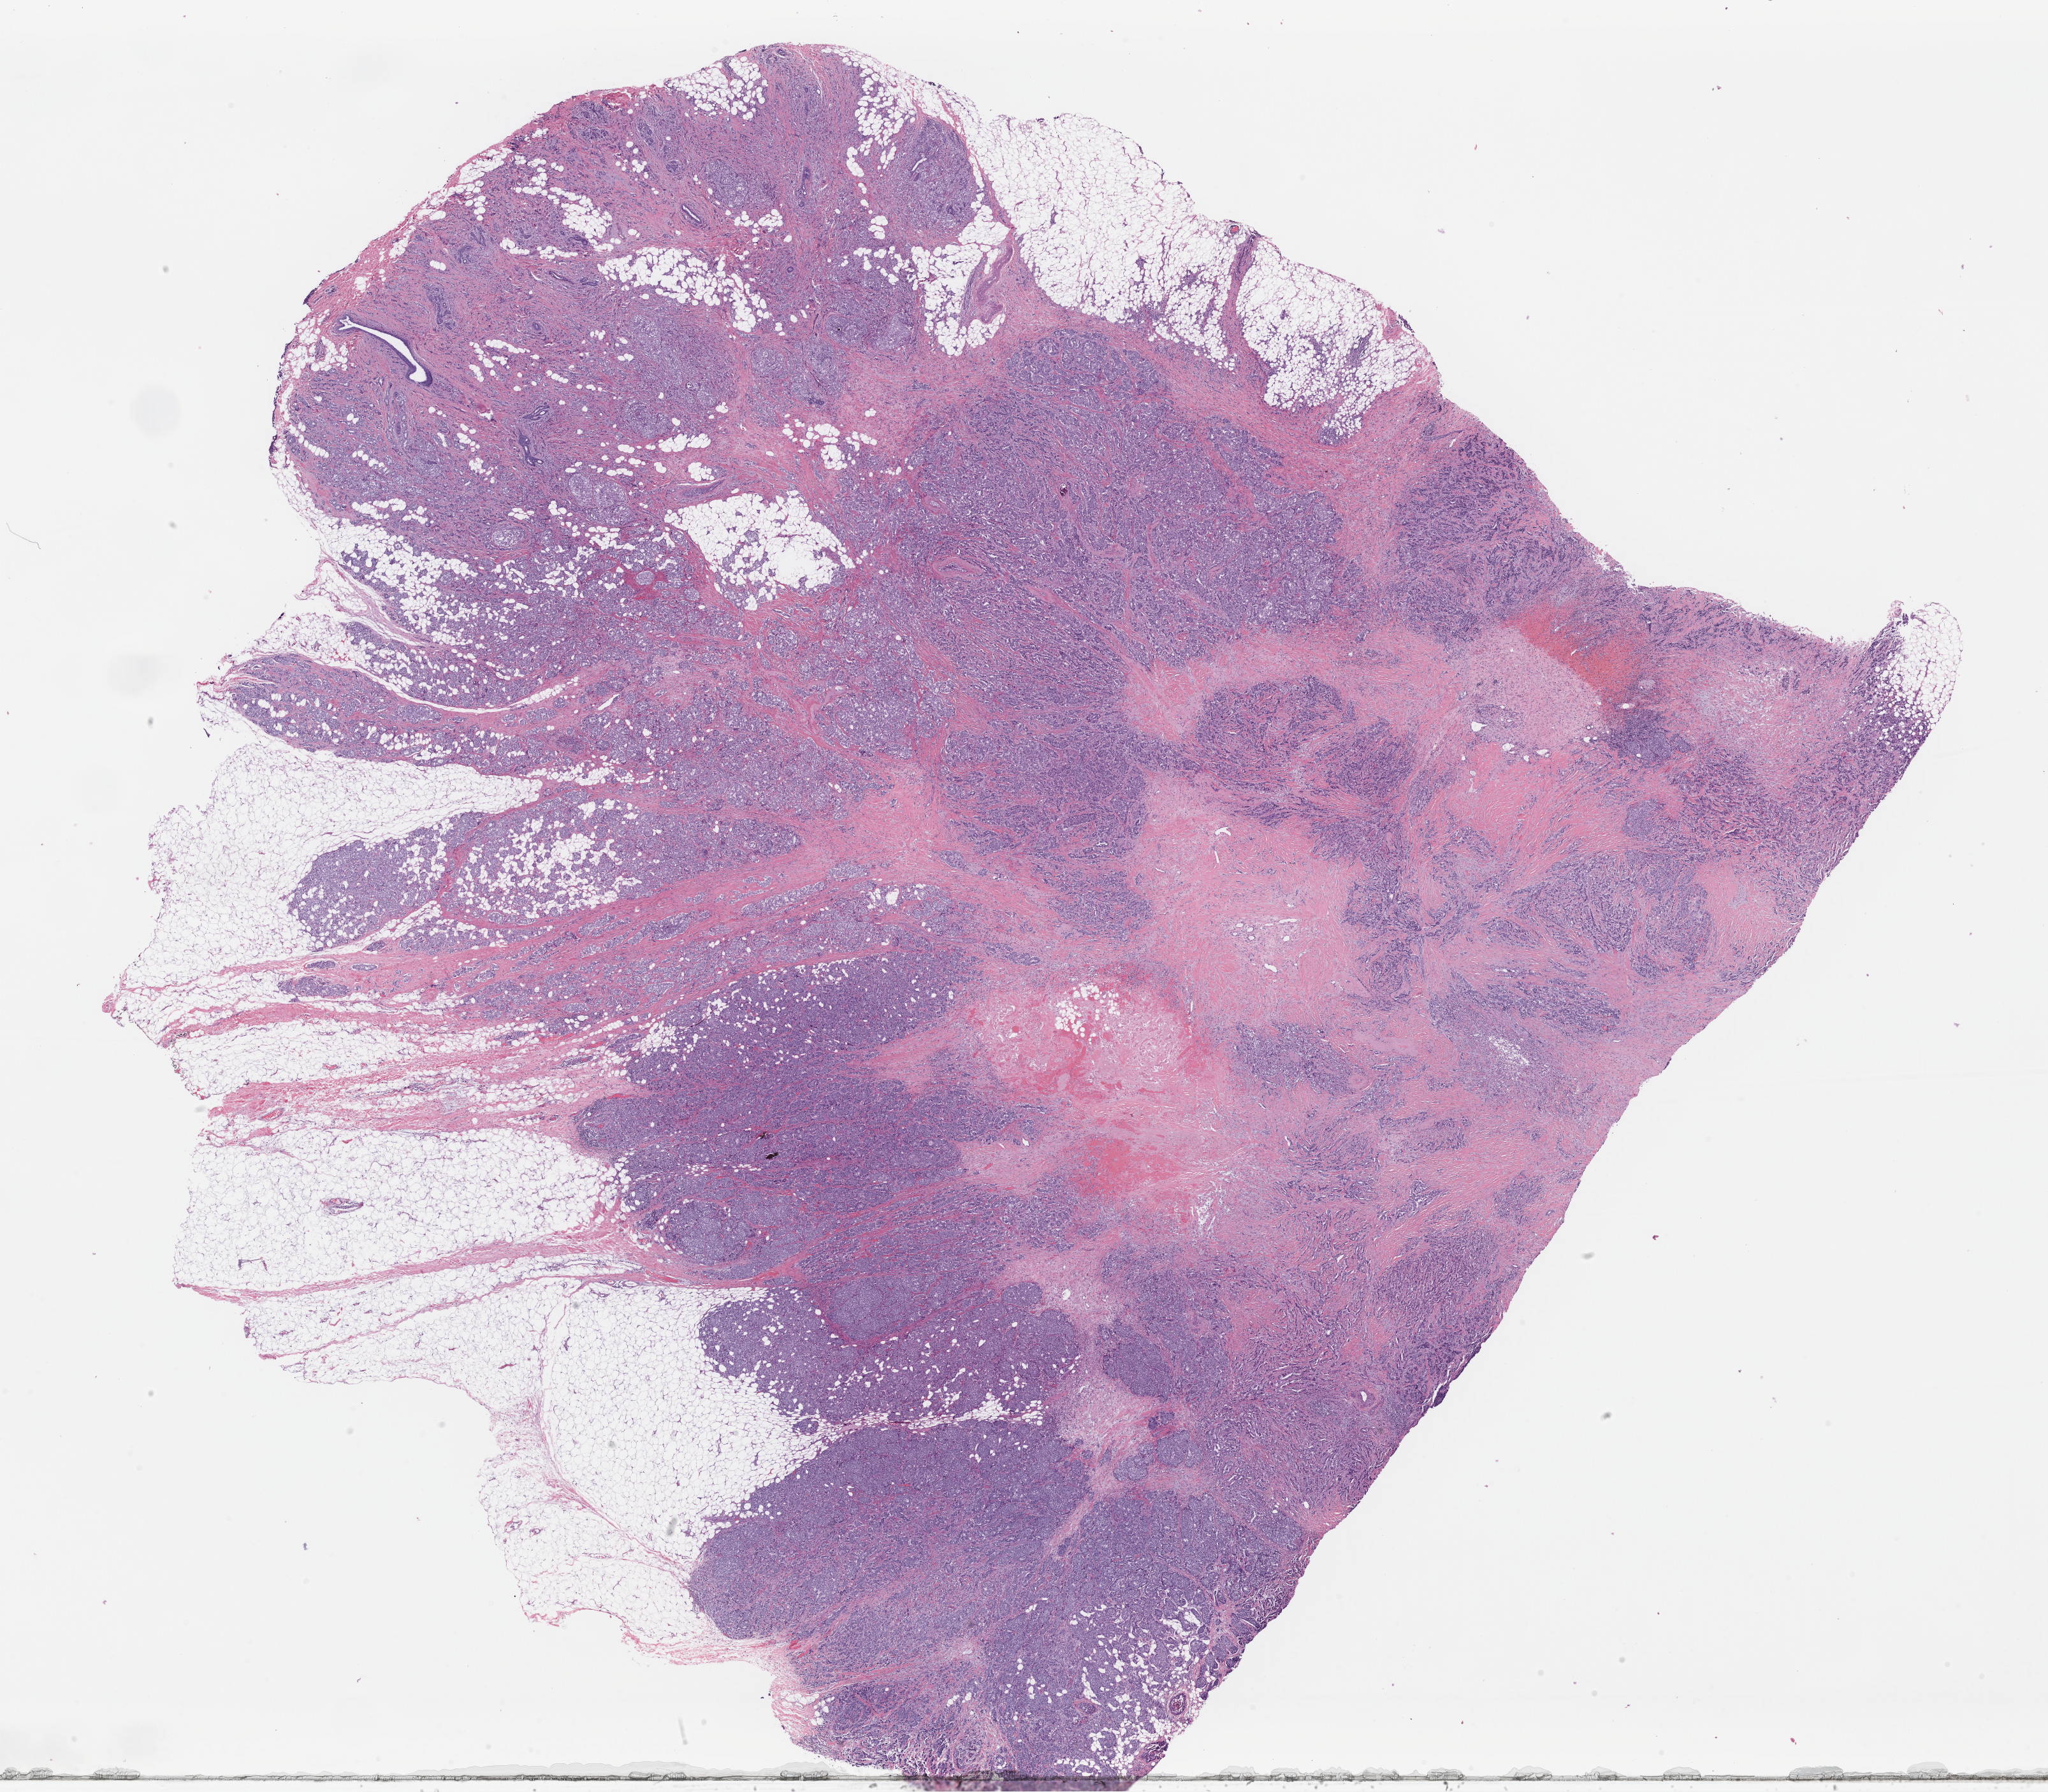
Hematoxylin and eosin (H&E) stained whole-slide image, low-resolution overview of the scanned area, about 25.4 x 22.2 mm. Formalin-fixed paraffin-embedded (FFPE) diagnostic section. Breast, primary tumour sample. Female patient; age at initial diagnosis 39 years.
TNM: T2 N1 M0. AJCC pathologic stage: IIB (7th edition). Histologic diagnosis: Infiltrating duct carcinoma, NOS.